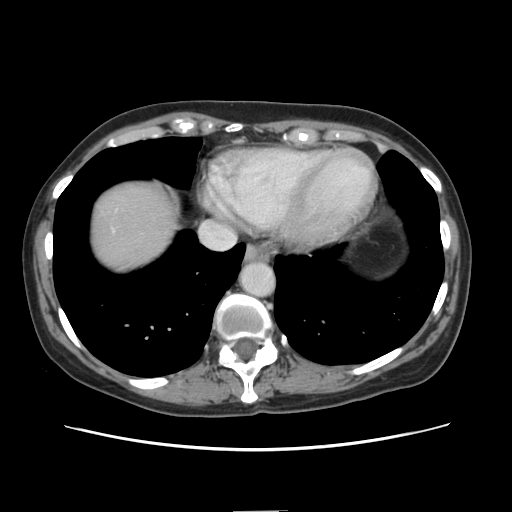
Contrast-enhanced abdominal CT, one axial slice; soft-tissue window (W 400 / L 40 HU); 2.5 mm slice thickness; 512 × 512 image matrix, field of view 350 × 350 mm. Female patient, age 63 years. From the clinical record (not read from this slice): diagnosis: colorectal cancer liver metastases, imaged before liver resection; multiple liver metastases: yes; largest metastasis: 3.2 cm; chemotherapy before resection: yes.
Annotated regions visible in this slice (expert manual segmentation):
- liver: bounding box [x1, y1, x2, y2] px = [91, 179, 176, 272]